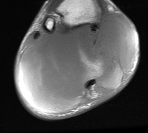
MRI of an extremity soft-tissue mass, one axial slice. Slice 20 of 76 in the series (ordered by position). MR volume resampled by the dataset authors to the PET/CT grid (not the native acquisition matrix). 3.27 mm slice thickness. 148 × 133 image matrix, field of view 145 × 130 mm. Male patient. Case-level facts recorded for this patient, not image findings: histological type: liposarcoma - round cell; grade: high; site of the primary tumour: right calf.
Outlined on this slice (expert contour drawn on MRI and transferred to this co-registered scan by the dataset authors):
- gross tumour volume (mass): box from (x=17, y=16) to (x=137, y=113) px